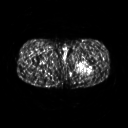
FDG PET of an extremity soft-tissue mass (from a PET/CT study), one axial slice. Slice 247 of 267 in the series (ordered by position). 3.27 mm slice thickness. 128 × 128 image matrix, field of view 500 × 500 mm. Patient: male, 27 years. Case-level facts recorded for this patient, not image findings: histological type: extraskeletal osteosarcoma; grade: high; site of the primary tumour: left adductur.
Outlined on this slice (expert contour drawn on MRI and transferred to this co-registered scan by the dataset authors):
- gross tumour volume (mass): box from (x=72, y=58) to (x=95, y=74) px